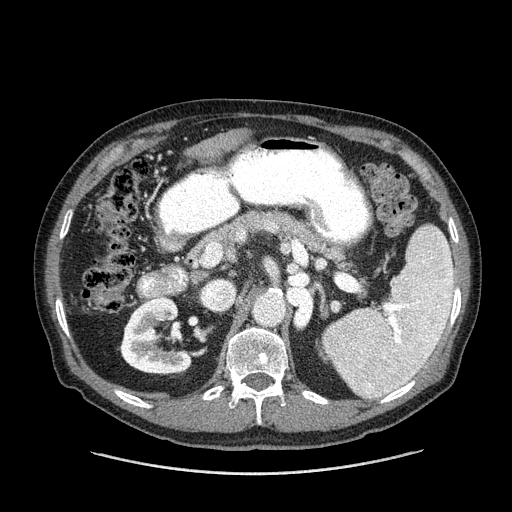
Contrast-enhanced abdominal CT (liver protocol), one axial slice. Slice 60 of 180 in the series (ordered by position). Reconstruction kernel STANDARD. 120 kVp. One of 2 acquisitions stored at this slice position. Soft-tissue window (W 400 / L 40 HU). 512 × 512 image matrix, field of view 420 × 420 mm. Case-level facts recorded for this patient, not image findings: diagnosis: hepatocellular carcinoma (patient treated with transarterial chemoembolisation; whether this scan precedes or follows treatment is not stated here); TNM stage (as recorded): Stage-II; Child-Pugh class: A; tumour differentiation: well differentiated.
Structures marked on this image (semi-automatic segmentation, software-assisted and operator-edited):
- liver parenchyma outside the tumour (the mass and vessels are separate outlines, so this box may not span the whole liver): bounding box [x1, y1, x2, y2] px = [196, 136, 236, 156]